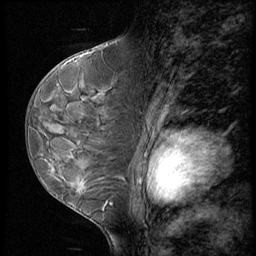
Breast MRI (dynamic contrast-enhanced), one sagittal slice. Position 35 of 60 along the scan axis. 3 images stored at this slice position (order not interpretable as contrast timing). 1.5 T. TE 4.2 ms, TR 8.9 ms. 256 × 256 image matrix. Female patient, age 50 years. From the clinical record (not read from this slice): setting: breast cancer imaged before/during neoadjuvant chemotherapy; receptor status: HR-positive, HER2-negative.
Annotated regions visible in this slice (semi-automatic segmentation, software-assisted and operator-edited):
- analysis volume of interest (the breast-tissue region the enhancement analysis was run in; not a lesion): bounding box <38,102,118,213> (left, top, right, bottom; pixels)
- tumour enhancement mask (voxels above the 140 % enhancement threshold inside the analysis volume of interest): <82,184,84,193>